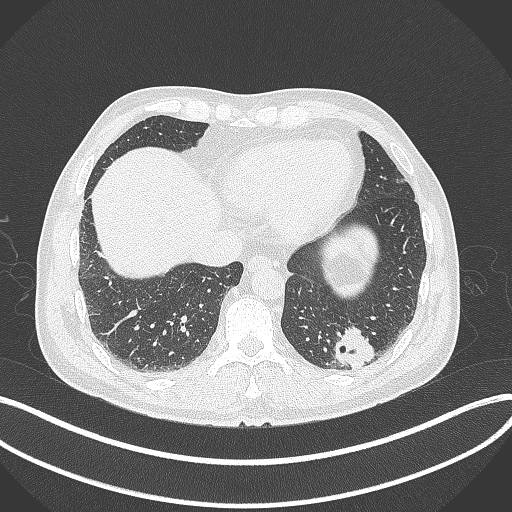
Chest CT, one axial slice; position 67 of 300 along the scan axis; 120 kVp; lung window (W 1500 / L -600 HU); 1 mm slice thickness; 512 × 512 image matrix. Patient: male, 54 years. From the clinical record (not read from this slice): clinical TNM (as recorded): T1c N0 M1.
Structures marked on this image (rectangle marked by the reading radiologist):
- lung tumour (recorded histology: adenocarcinoma): bounding box [x1, y1, x2, y2] px = [332, 325, 376, 374]